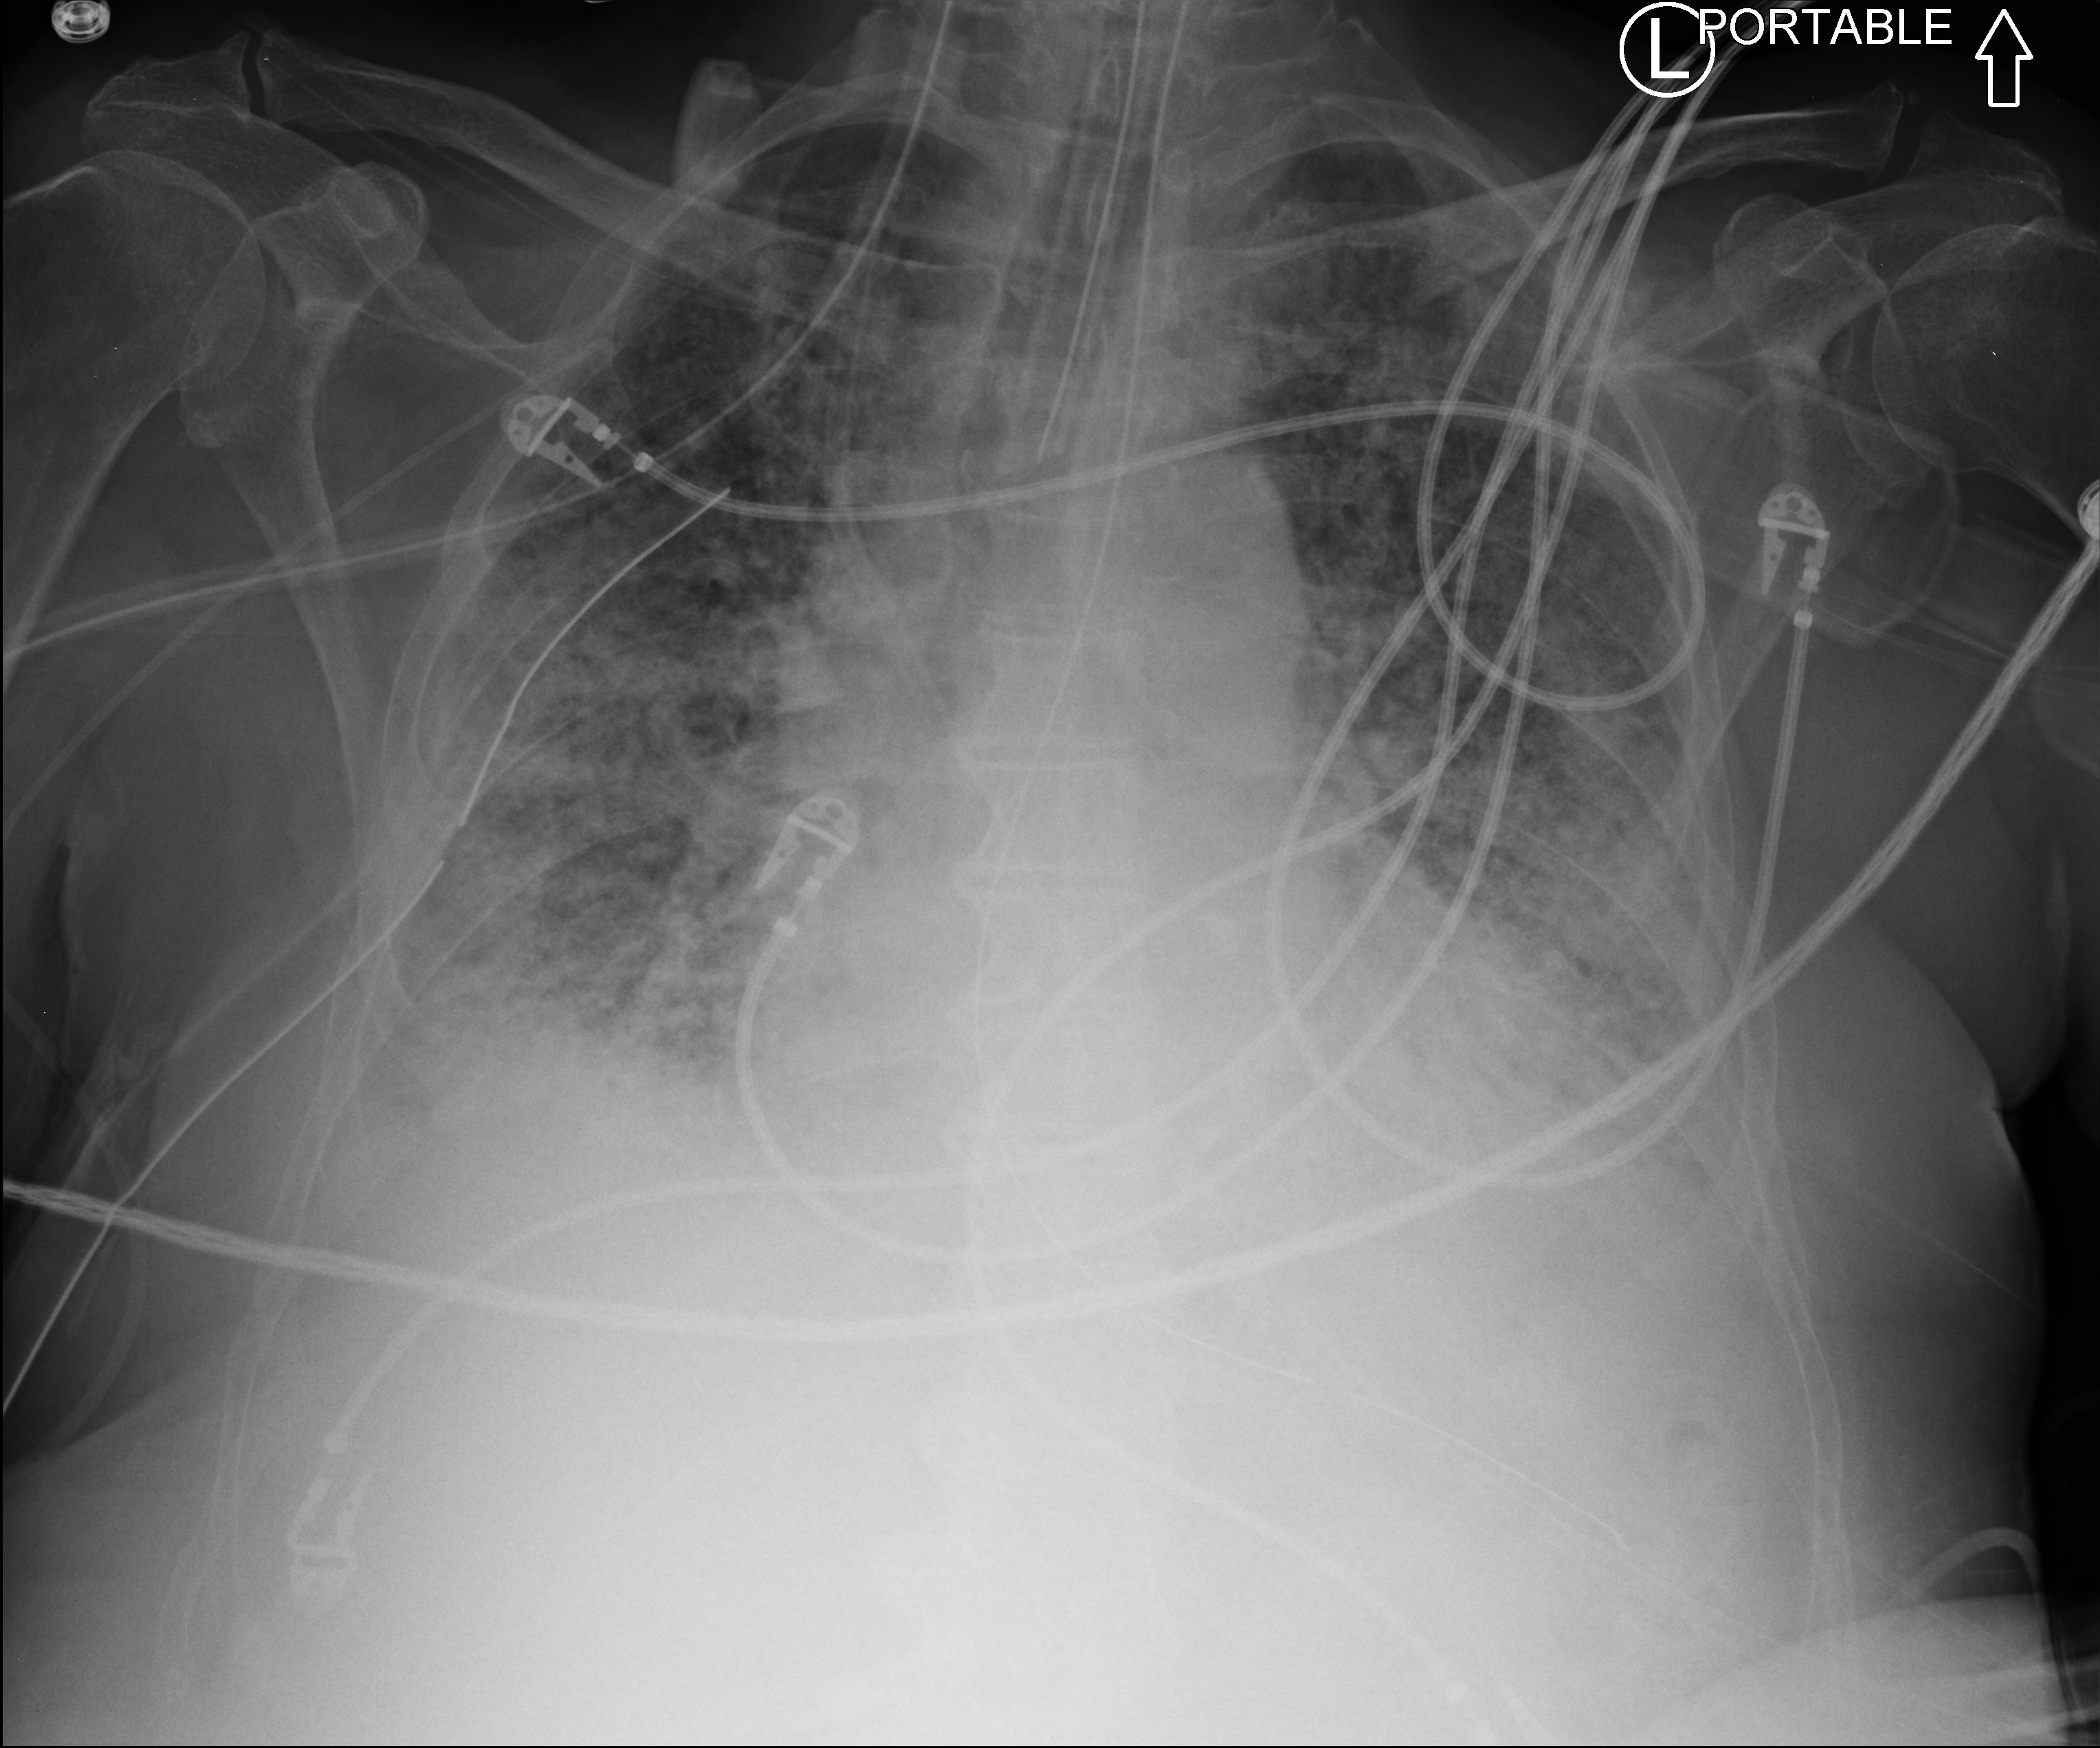
Chest X-ray (portable). Patient hospitalised with COVID-19; male, aged 75–90 years.
From the hospital-stay record, not from the radiograph (when in the stay this image was taken is not recorded): admitted to intensive care during this hospital stay: yes; mechanically ventilated during this hospital stay: yes.